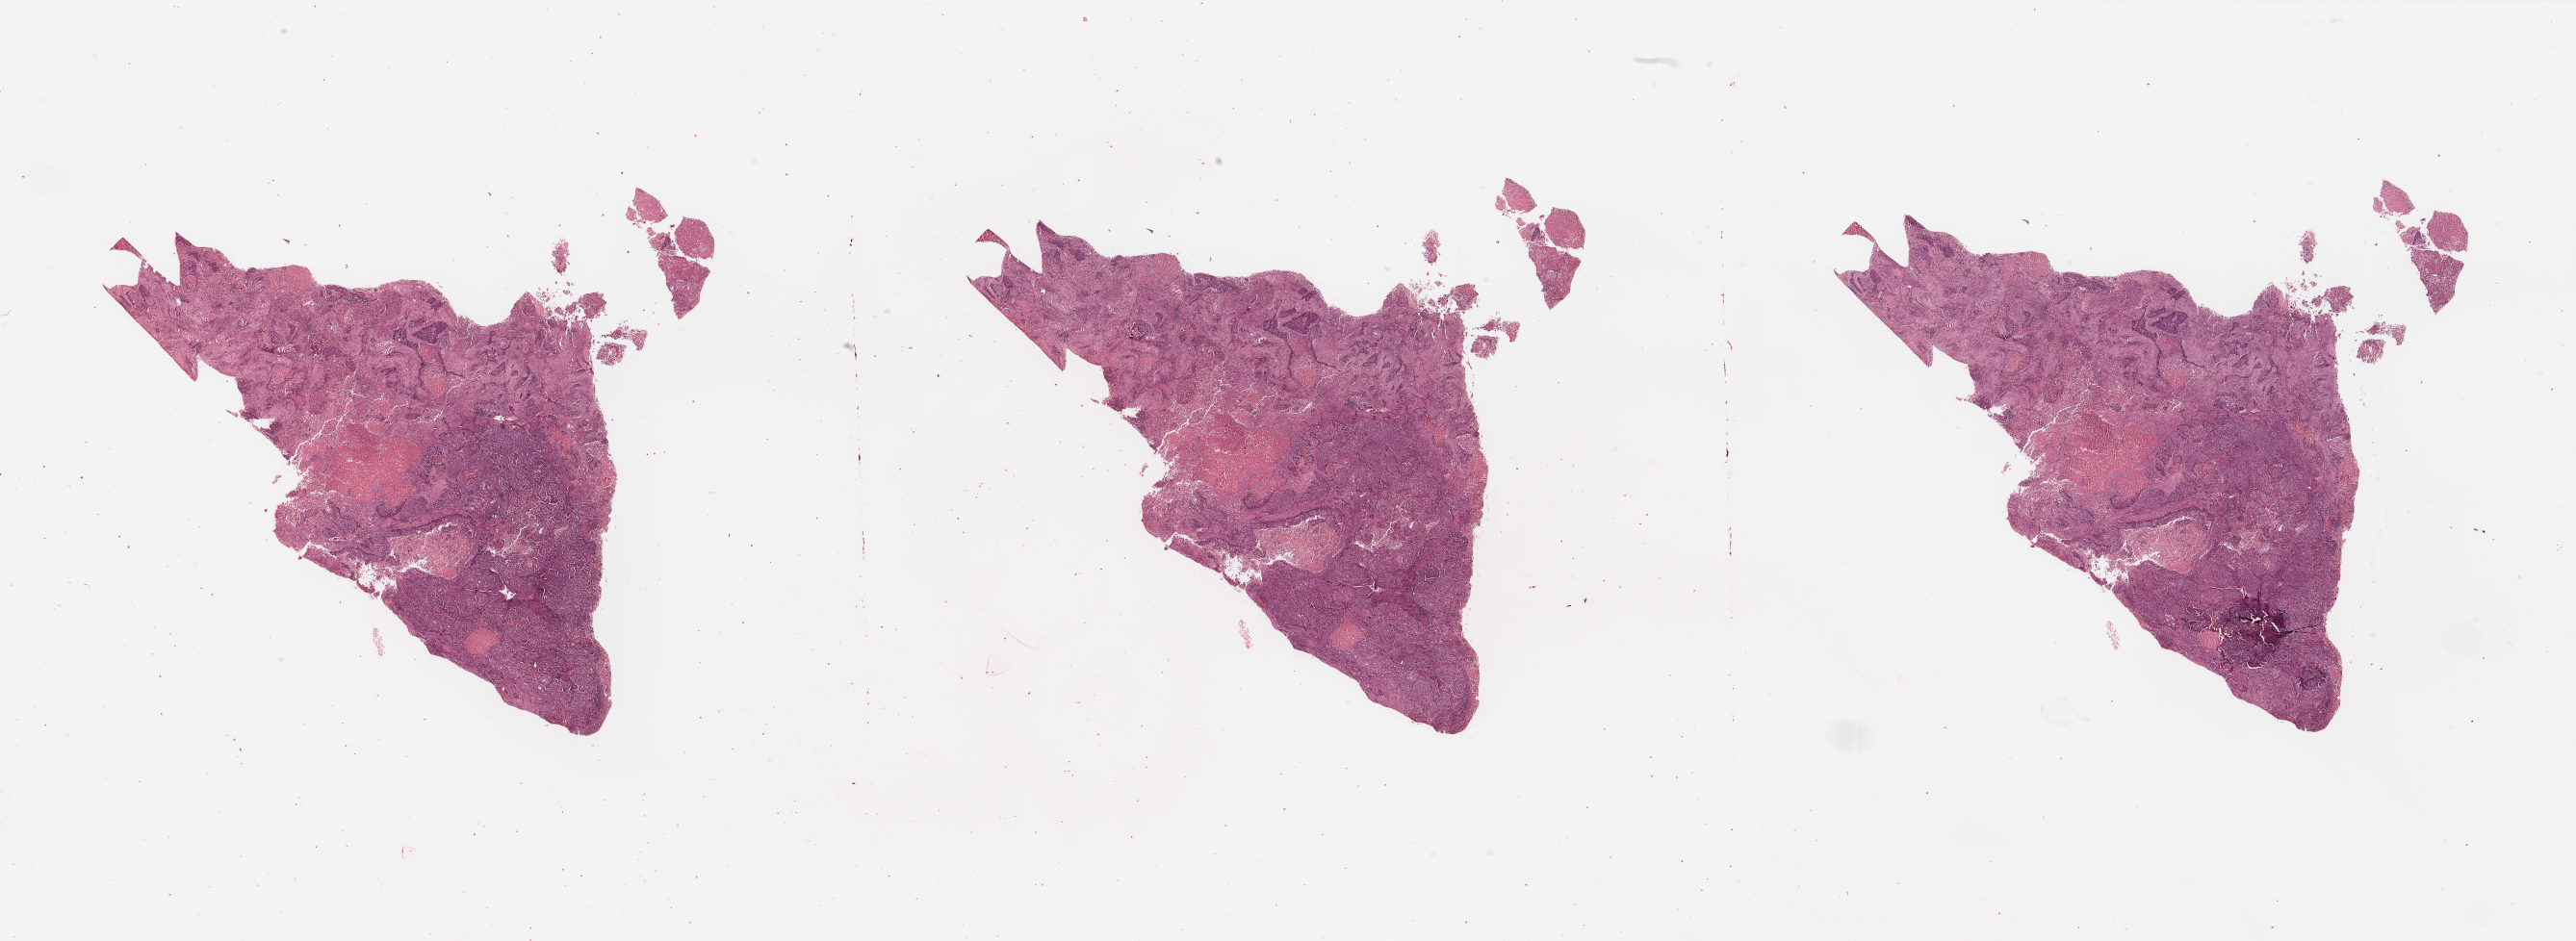
Whole-slide histology image, H&E, low-resolution overview of the scanned area, about 42.3 x 15.5 mm, head and neck, tissue type not recorded. Patient: male, age 64 years.
Patient diagnosis: Squamous cell carcinoma, NOS (larynx, NOS).